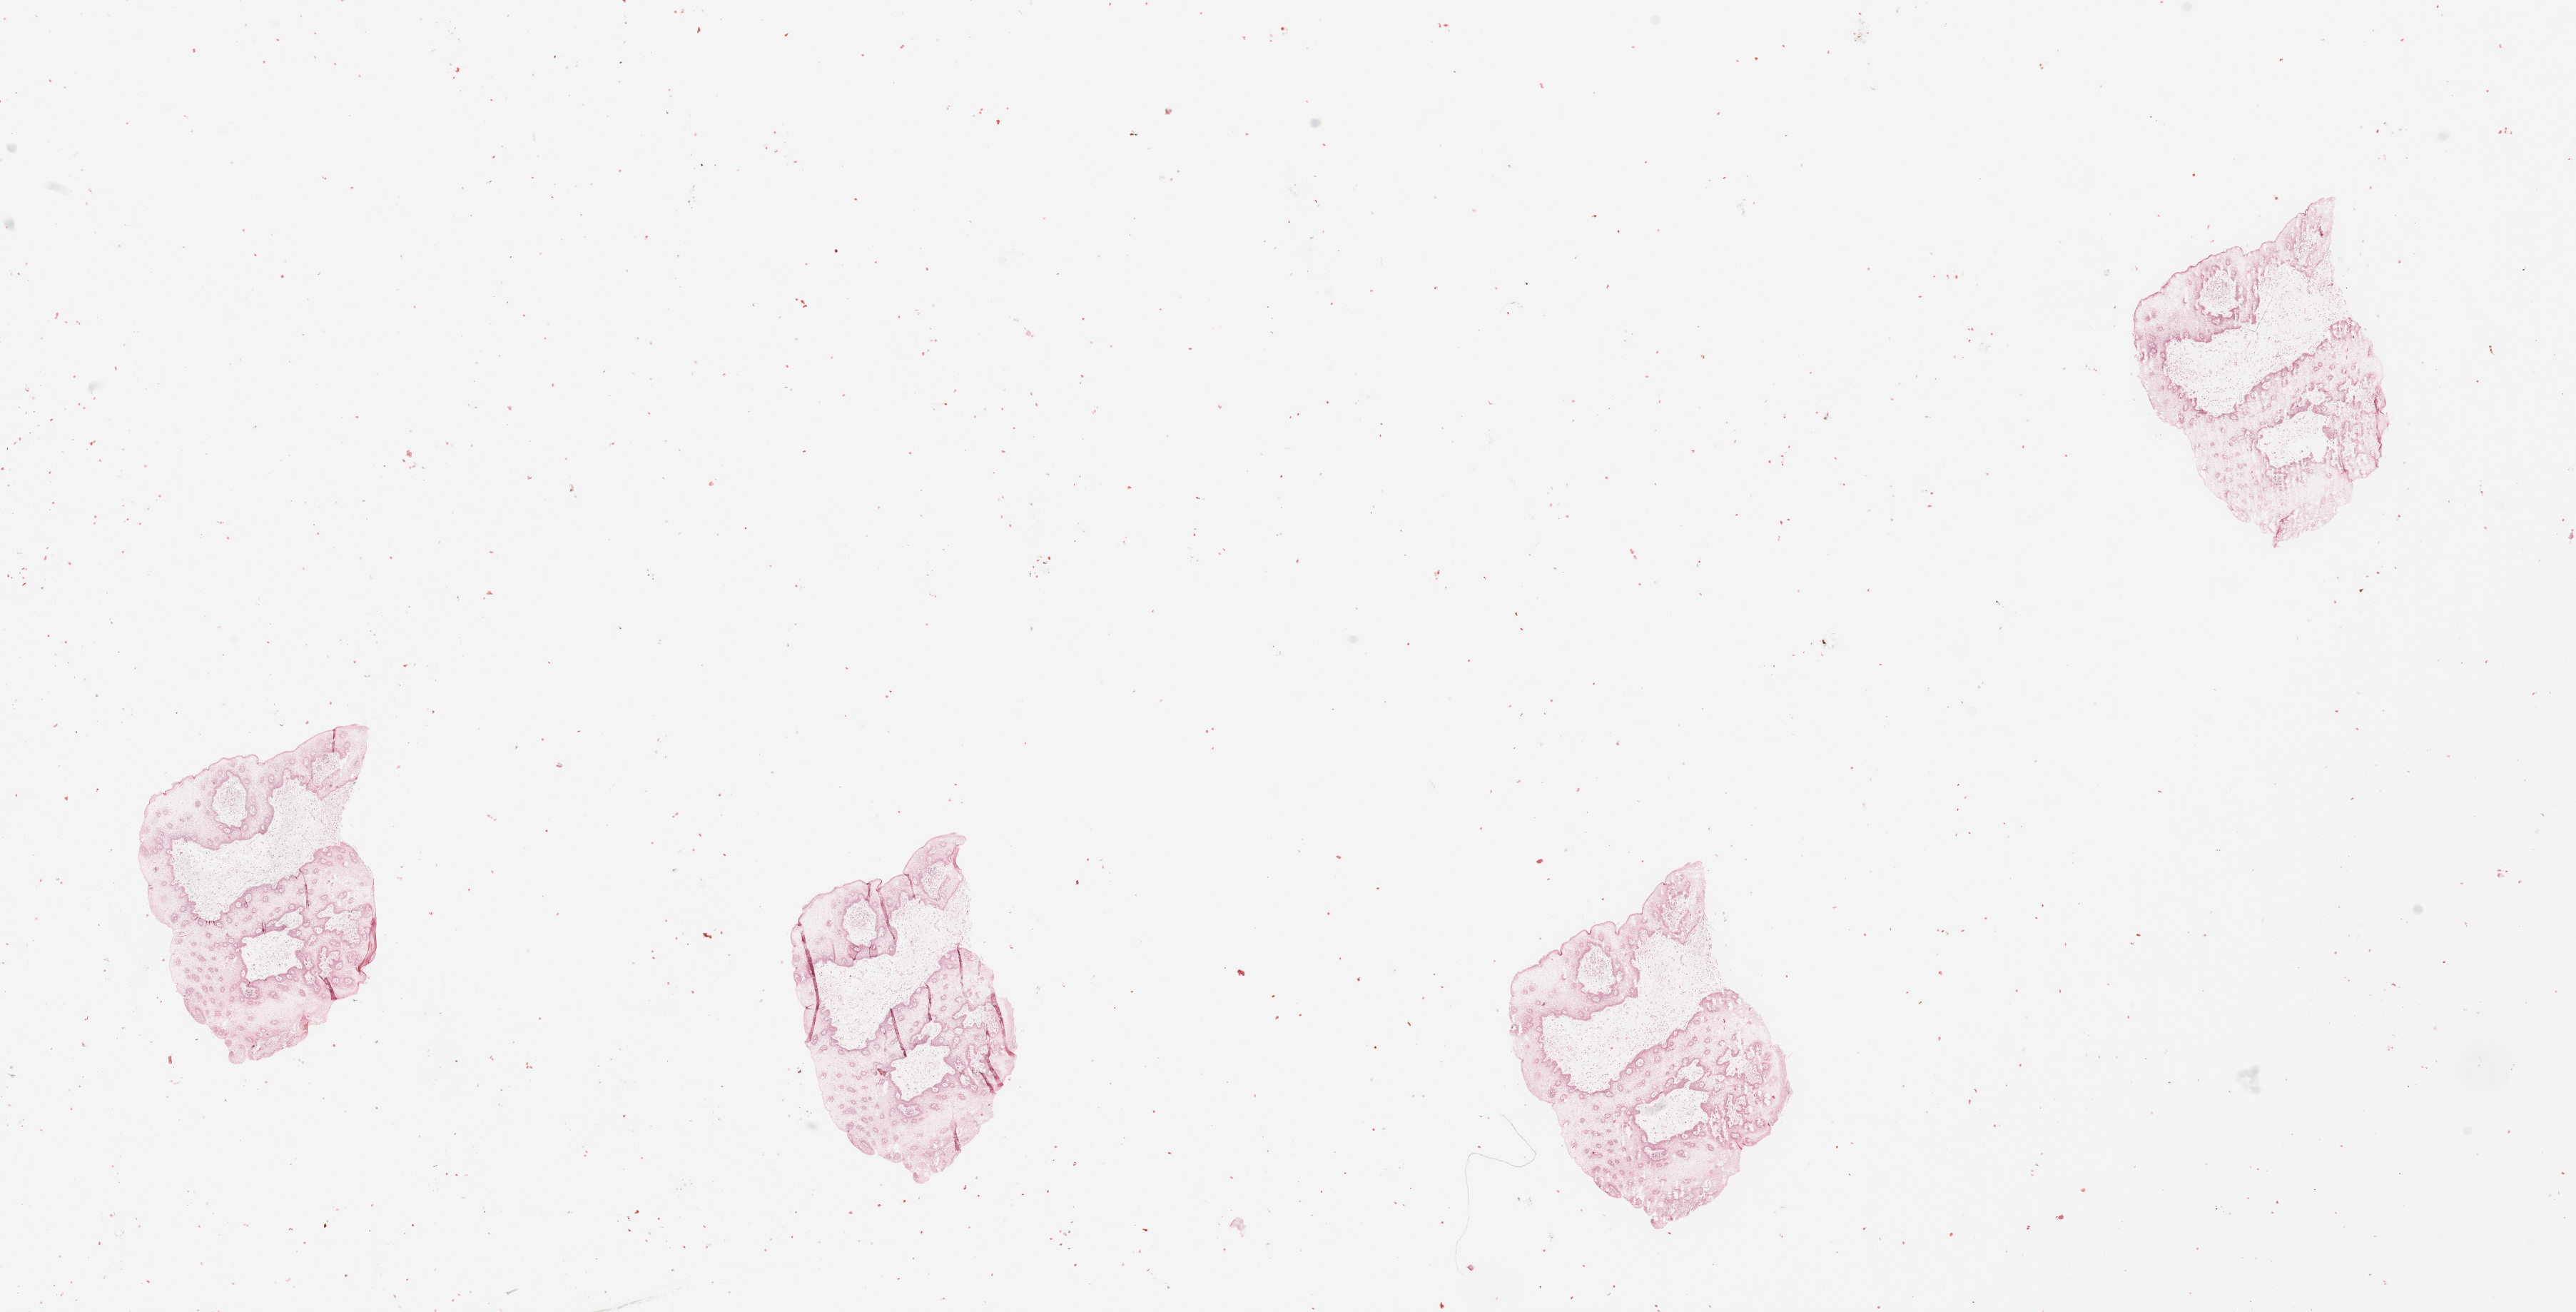
H&E whole-slide image, whole scanned area (about 28.5 x 14.5 mm, from a 20x scan) shown as a low-resolution overview, normal (non-tumour) tissue sample, sampled site: tongue. Patient: male, age 64 years.
This section: normal (non-tumour) tissue from the same patient. Patient diagnosis: Squamous cell carcinoma, NOS (tongue, NOS).